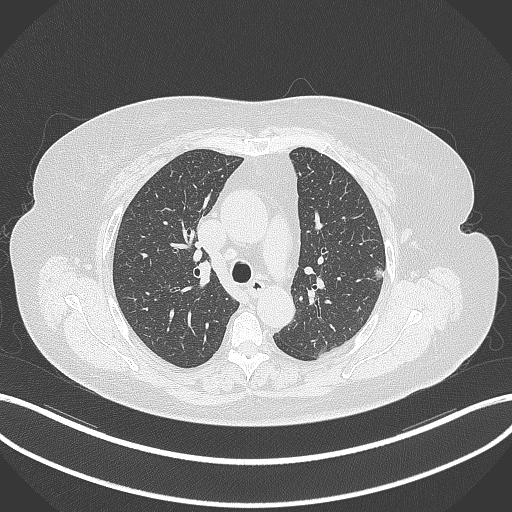
Chest CT, one axial slice. Reconstruction kernel B70f. 120 kVp. Lung window (W 1500 / L -600 HU). 1 mm slice thickness. 512 × 512 image matrix. Female patient, age 70 years. From the clinical record (not read from this slice): clinical TNM (as recorded): T1c N0 M0.
Structures marked on this image (bounding box drawn by a radiologist):
- lung tumour (recorded histology: adenocarcinoma): bounding box (x1, y1, x2, y2) in pixels: (369, 261, 386, 281)